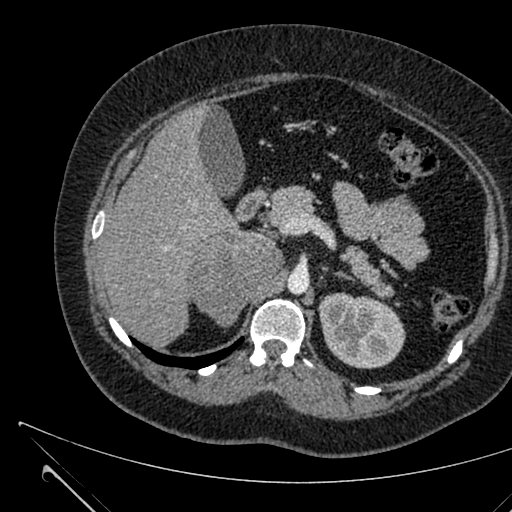
Contrast-enhanced abdominal CT, one axial slice. Slice 419 of 731 in the series (ordered by position). Intravenous contrast given. Soft-tissue window (W 400 / L 40 HU). 1 mm slice thickness. 512 × 512 image matrix. Patient: female, 36 years. Case-level facts recorded for this patient, not image findings: diagnosis: adrenocortical carcinoma; tumour side: right adrenal; tumour size at pathology: 10 cm.
Structures marked on this image (semi-automatically segmented with operator editing):
- mass: bounding box <187,232,282,326> (left, top, right, bottom; pixels)